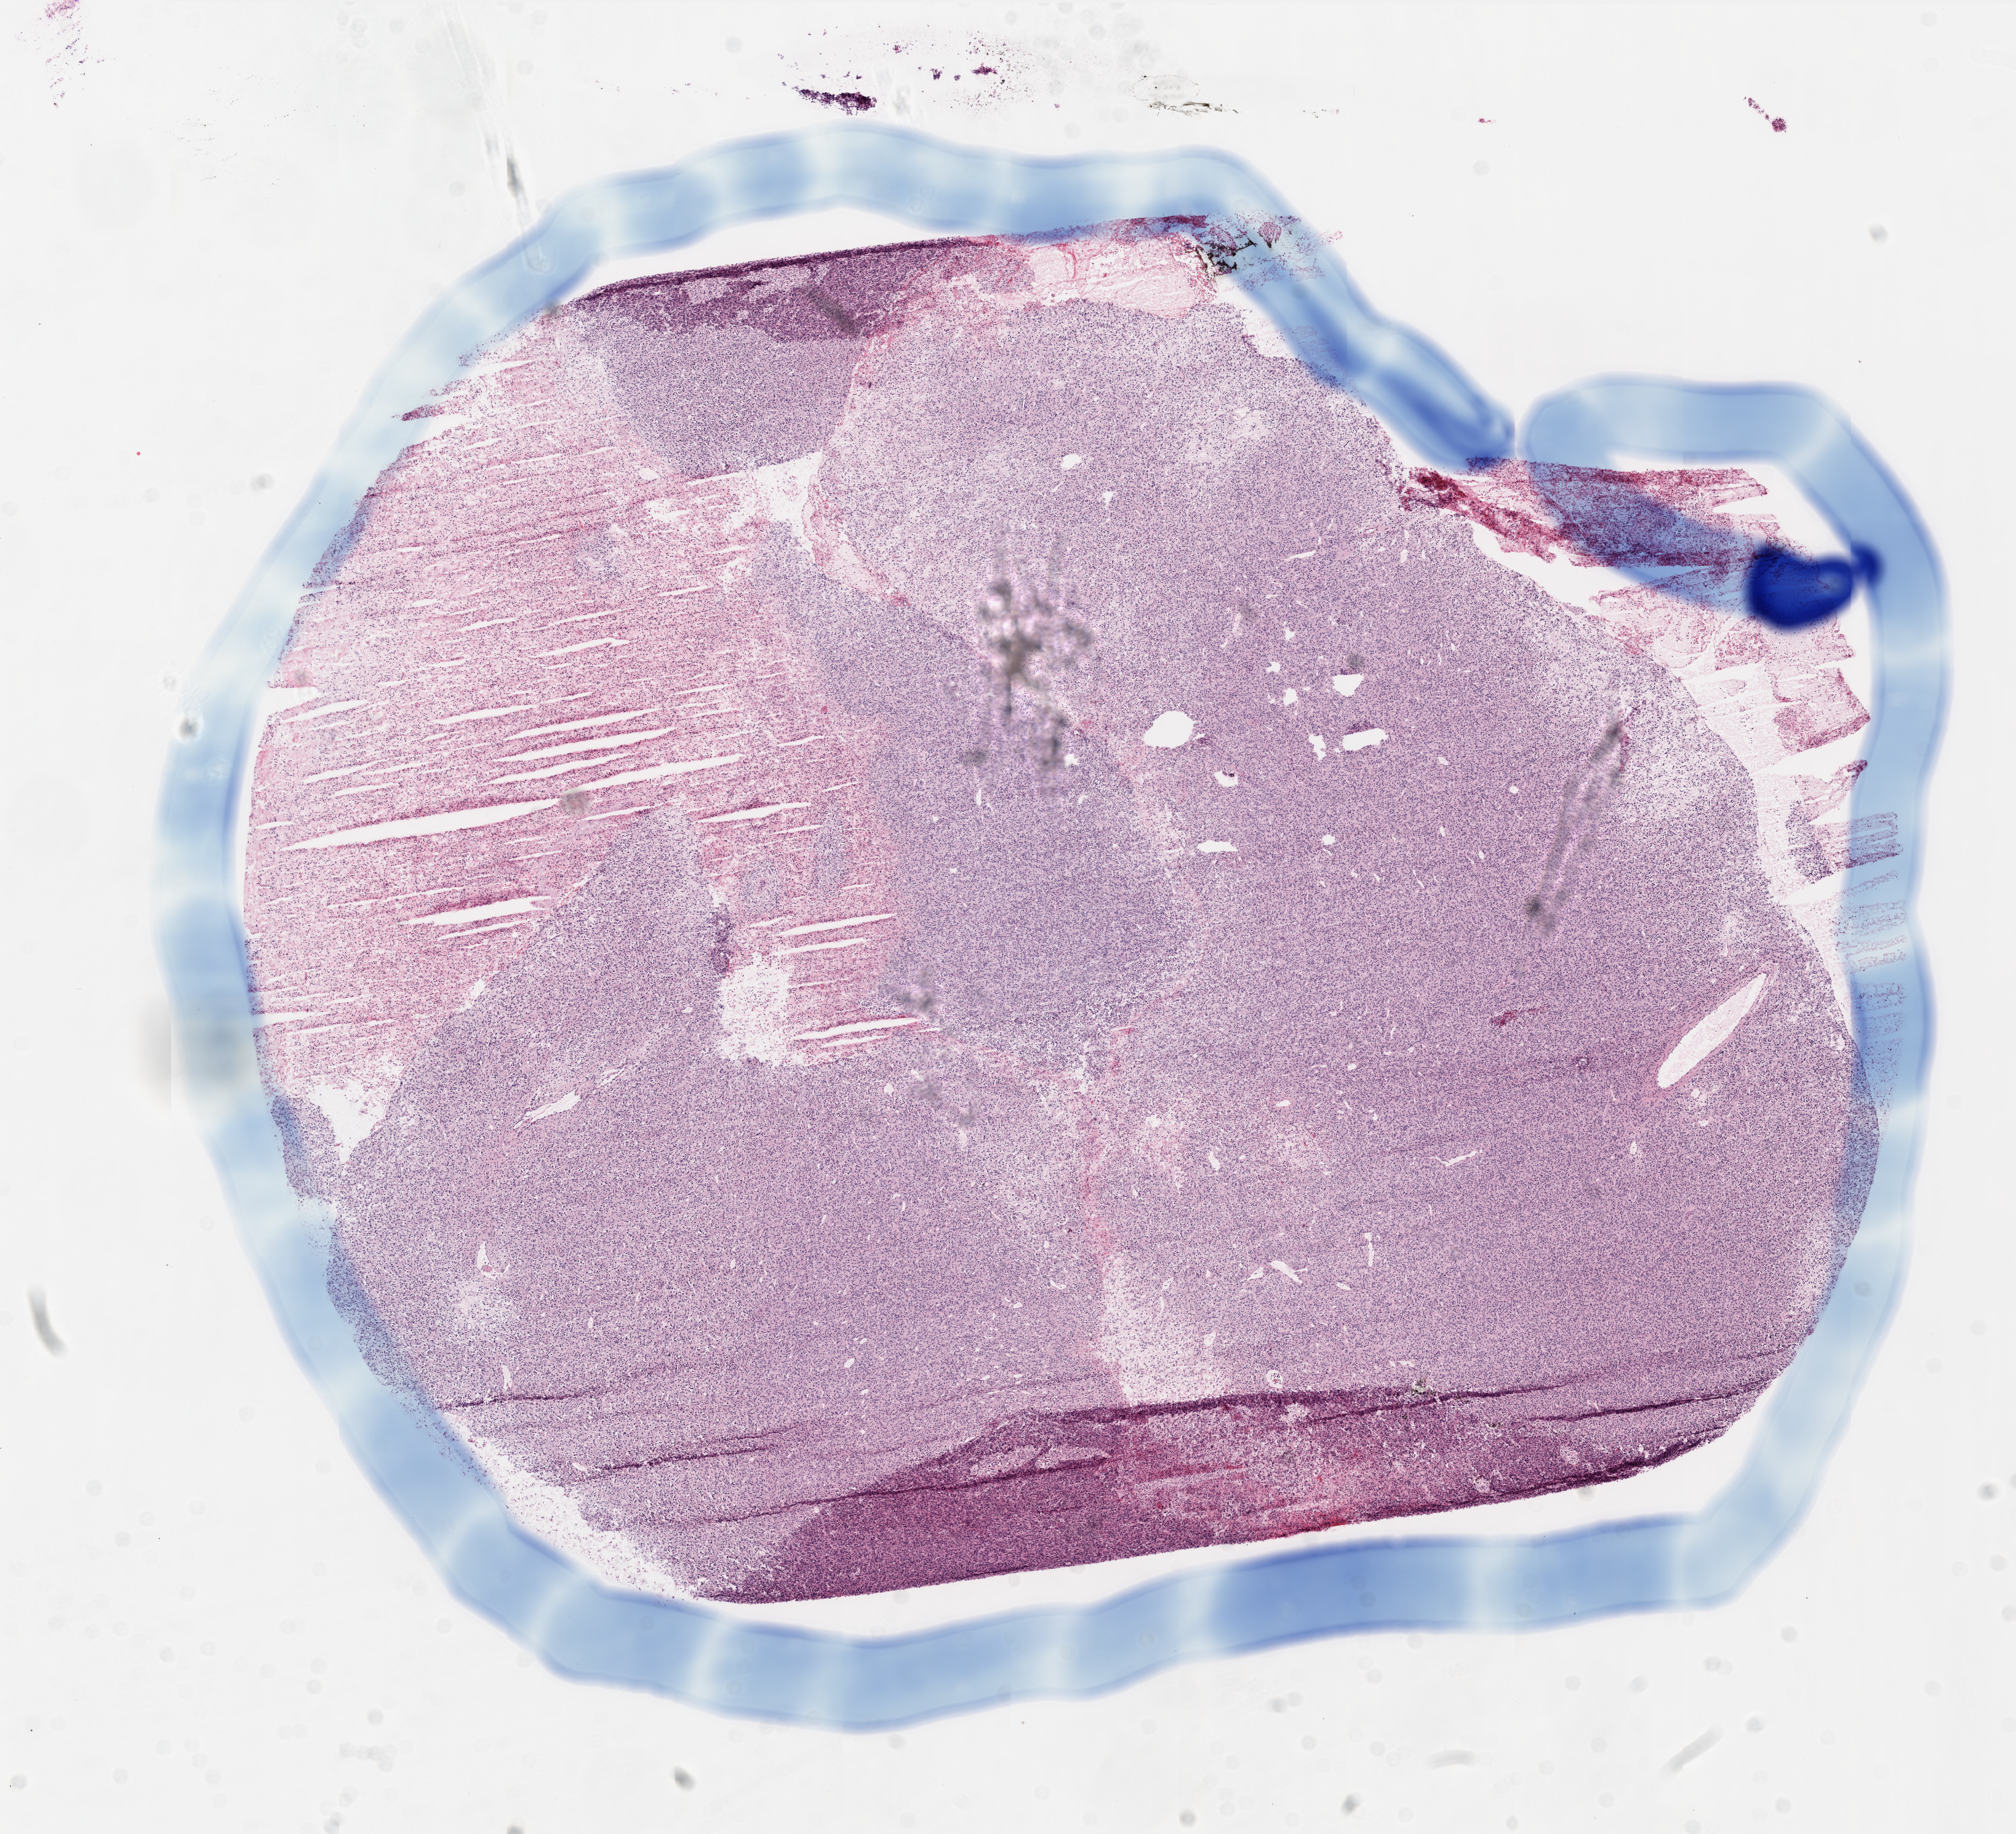
Digitized H&E tissue section (whole slide) — shown as a low-resolution overview of the whole scanned area (about 12.0 x 10.9 mm, acquisition: 20x scan). Frozen section from the top of the tissue portion. Sample: primary tumour, brain. Patient: female, age at initial diagnosis 53 years. Pathologist review of this section (percent, as recorded): tumour cells 80%, tumour nuclei 100%, normal cells 0%, stromal cells 0%, necrosis 20%. Infiltration values recorded for this section: lymphocyte infiltration 0%, monocyte infiltration 0%, neutrophil infiltration 0%.
Pathologic diagnosis: Glioblastoma.